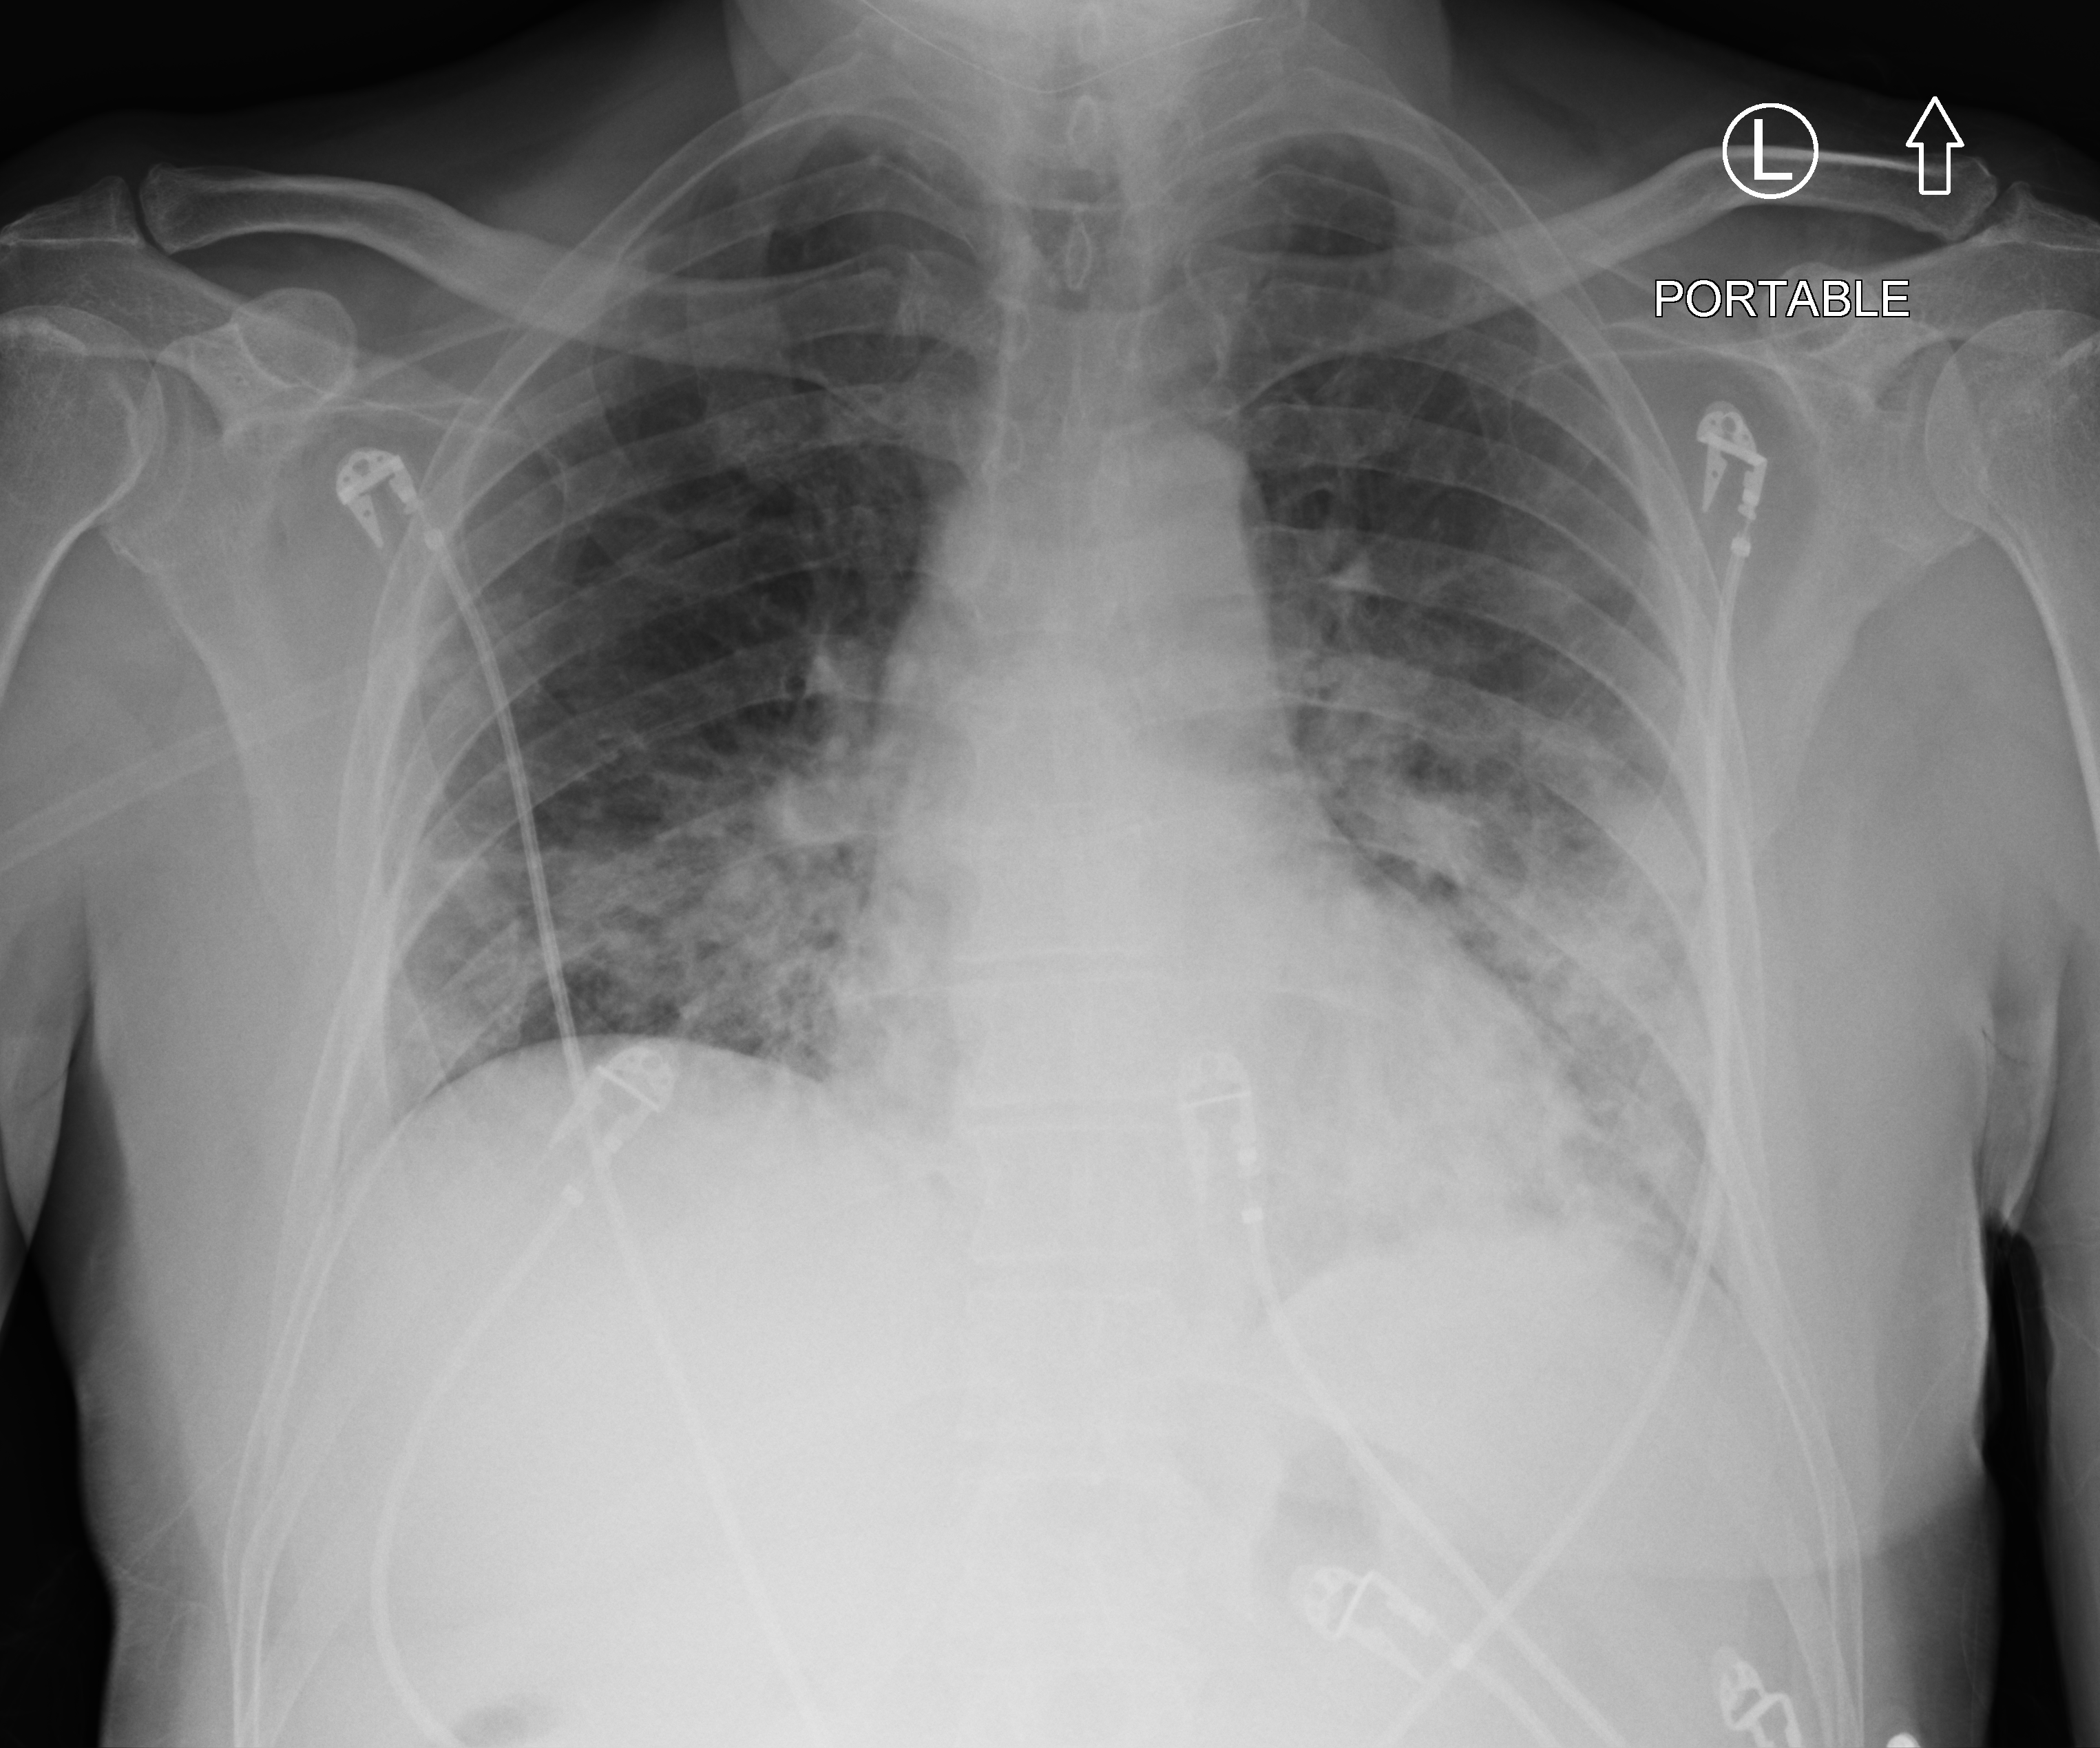
Chest X-ray (portable), anteroposterior (AP) projection. Male patient hospitalised with COVID-19, age 60–74 years.
Hospital-stay facts (about this admission, not read from this image; timing relative to this image not recorded):
- admitted to intensive care during this hospital stay: no
- mechanically ventilated during this hospital stay: no